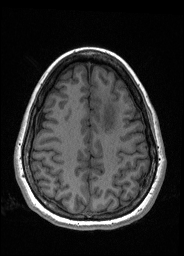
Pre-operative brain MRI before brain-tumour surgery, one axial slice; T1-weighted post-contrast; 184 × 256 image matrix, field of view 180 × 250 mm. Case-level facts recorded for this patient, not image findings: histopathology: Oligodendroglioma; WHO grade: 2; IDH mutation: yes; tumour location: Left Frontal.
Outlined on this slice (outlined manually by an expert reader):
- tumour: bounding box <100,97,118,133> (left, top, right, bottom; pixels)